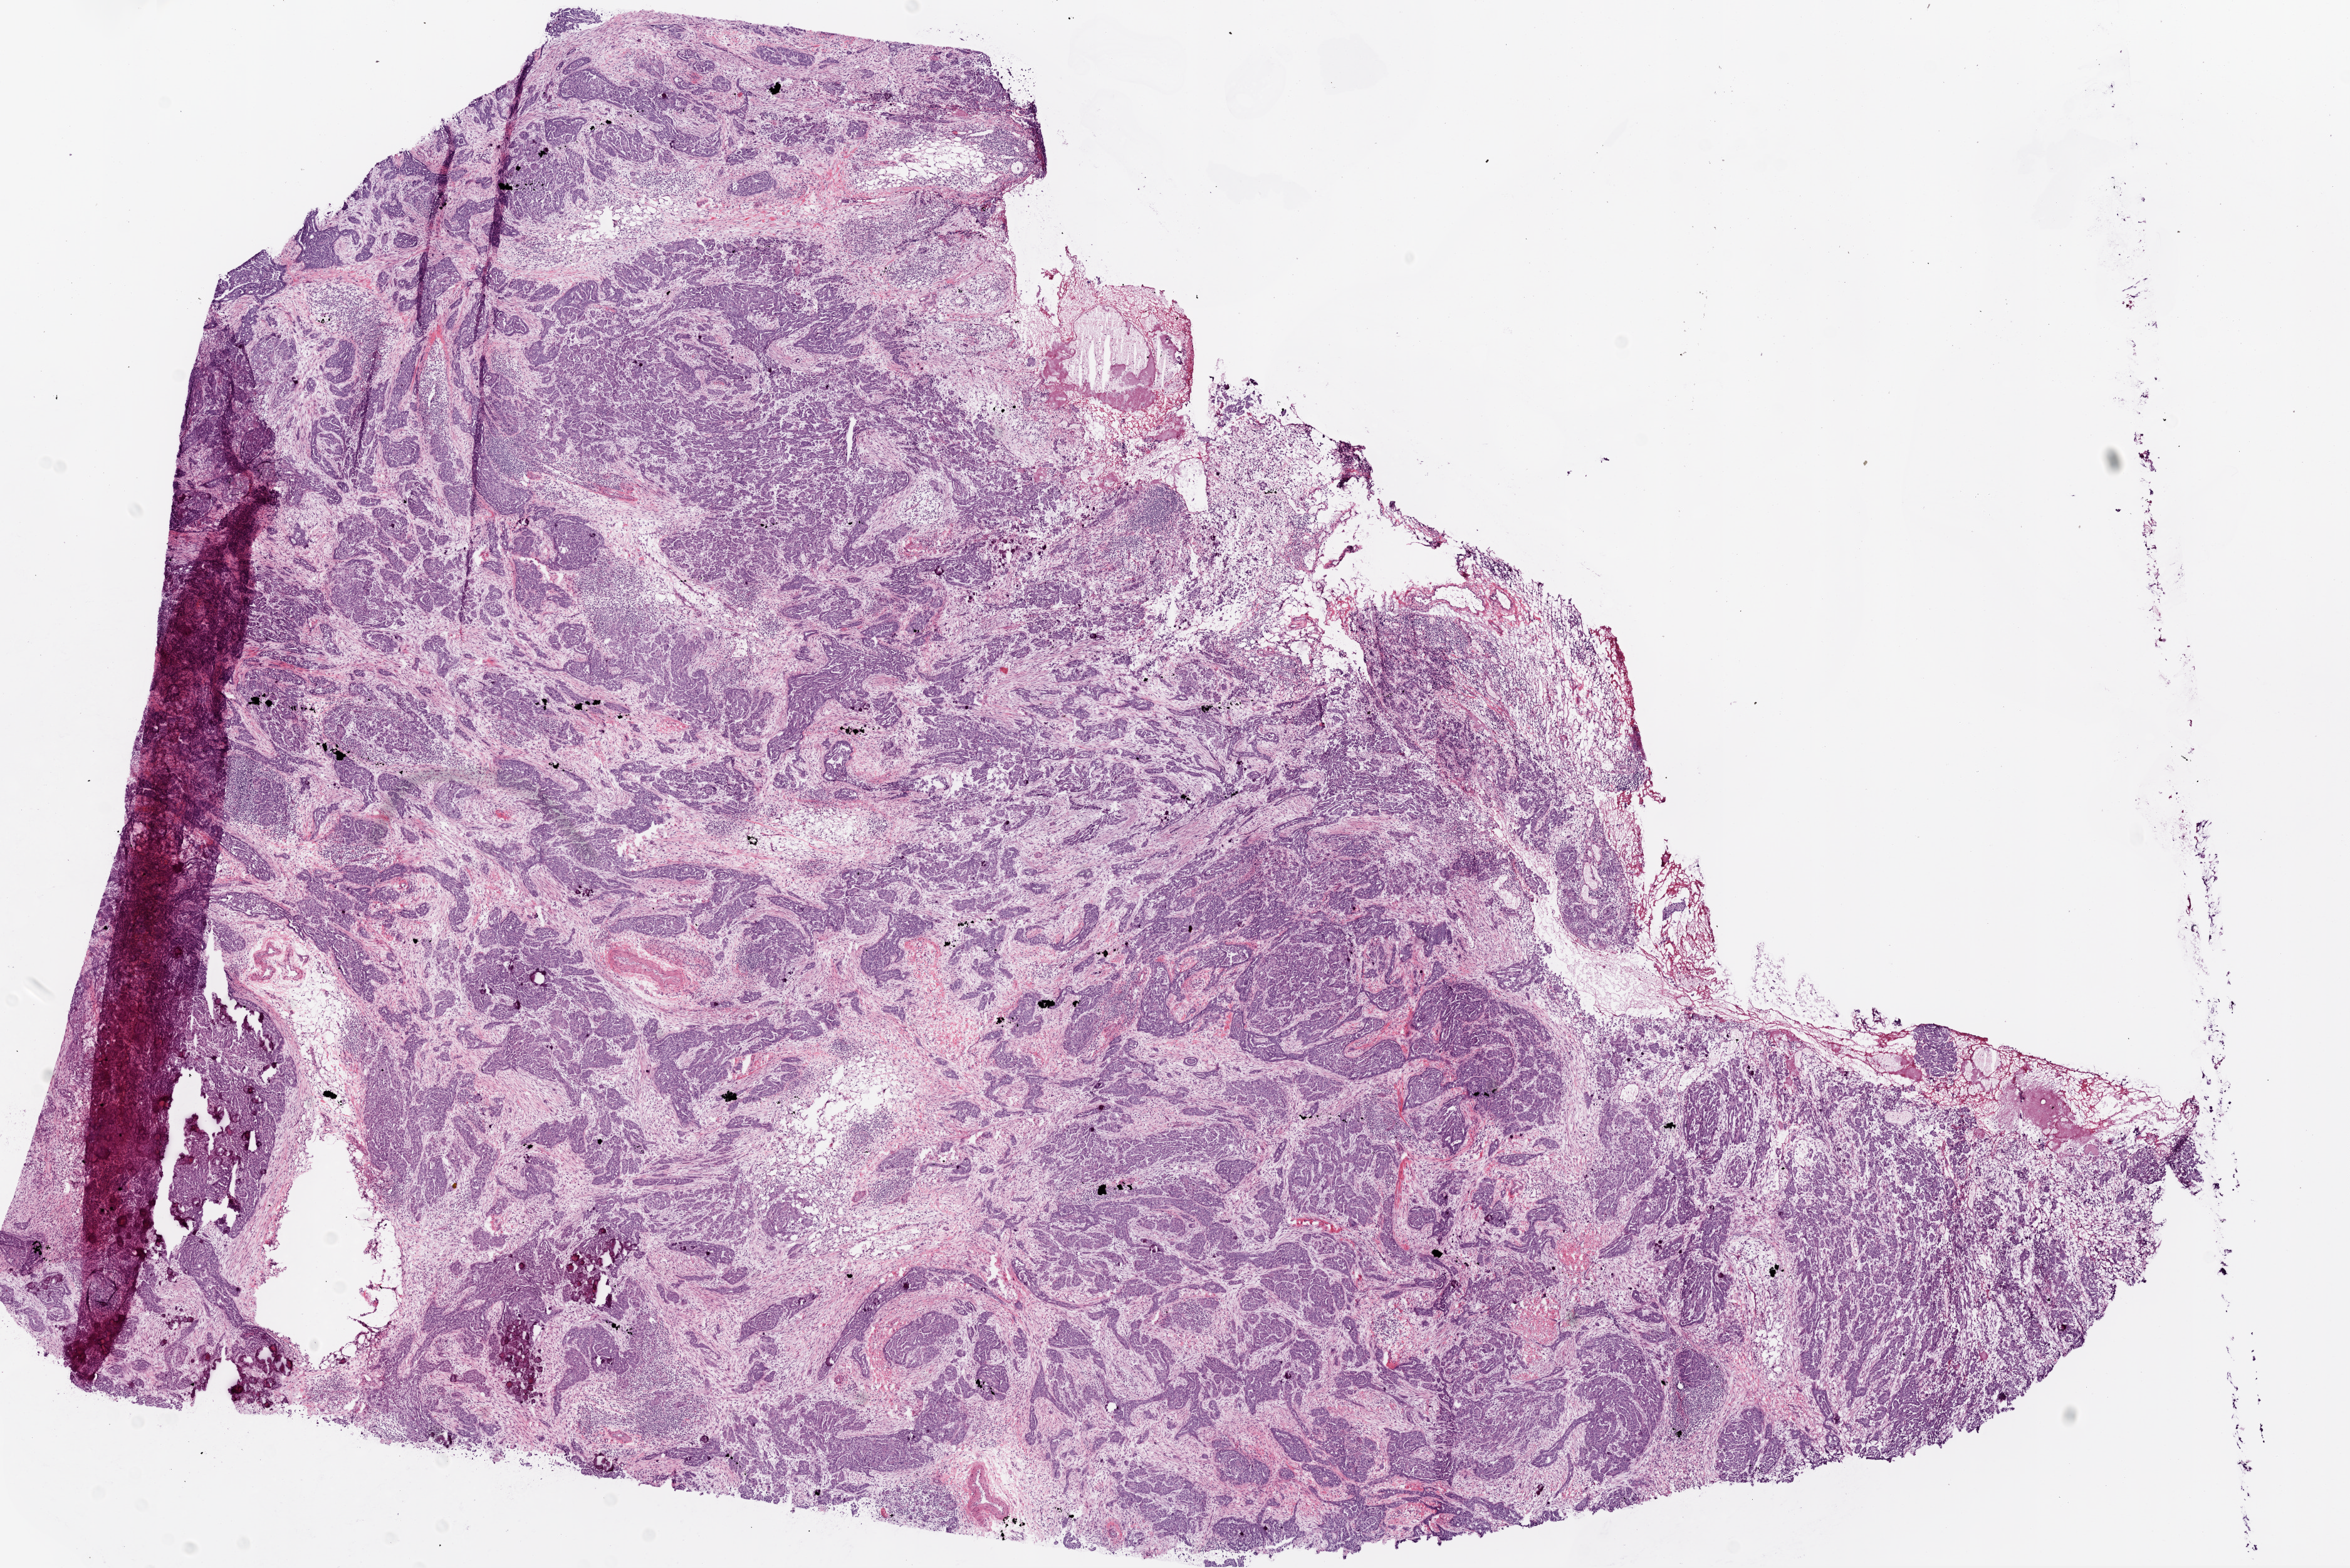
Digitized H&E tissue section (whole slide), a low-resolution overview of the entire scanned area, about 15.0 x 10.0 mm (acquisition: 20x scan); frozen section; ovary, primary tumour sample. Patient: female, age at initial diagnosis 52 years. Histologic grade: G3 (poorly differentiated). Slide review estimates, as recorded: tumour cells 90%, tumour nuclei 90%, normal cells 0%, stromal cells 10%, necrosis 0%.
Diagnosis: Serous cystadenocarcinoma, NOS. Laterality: bilateral. FIGO stage: IIIC.